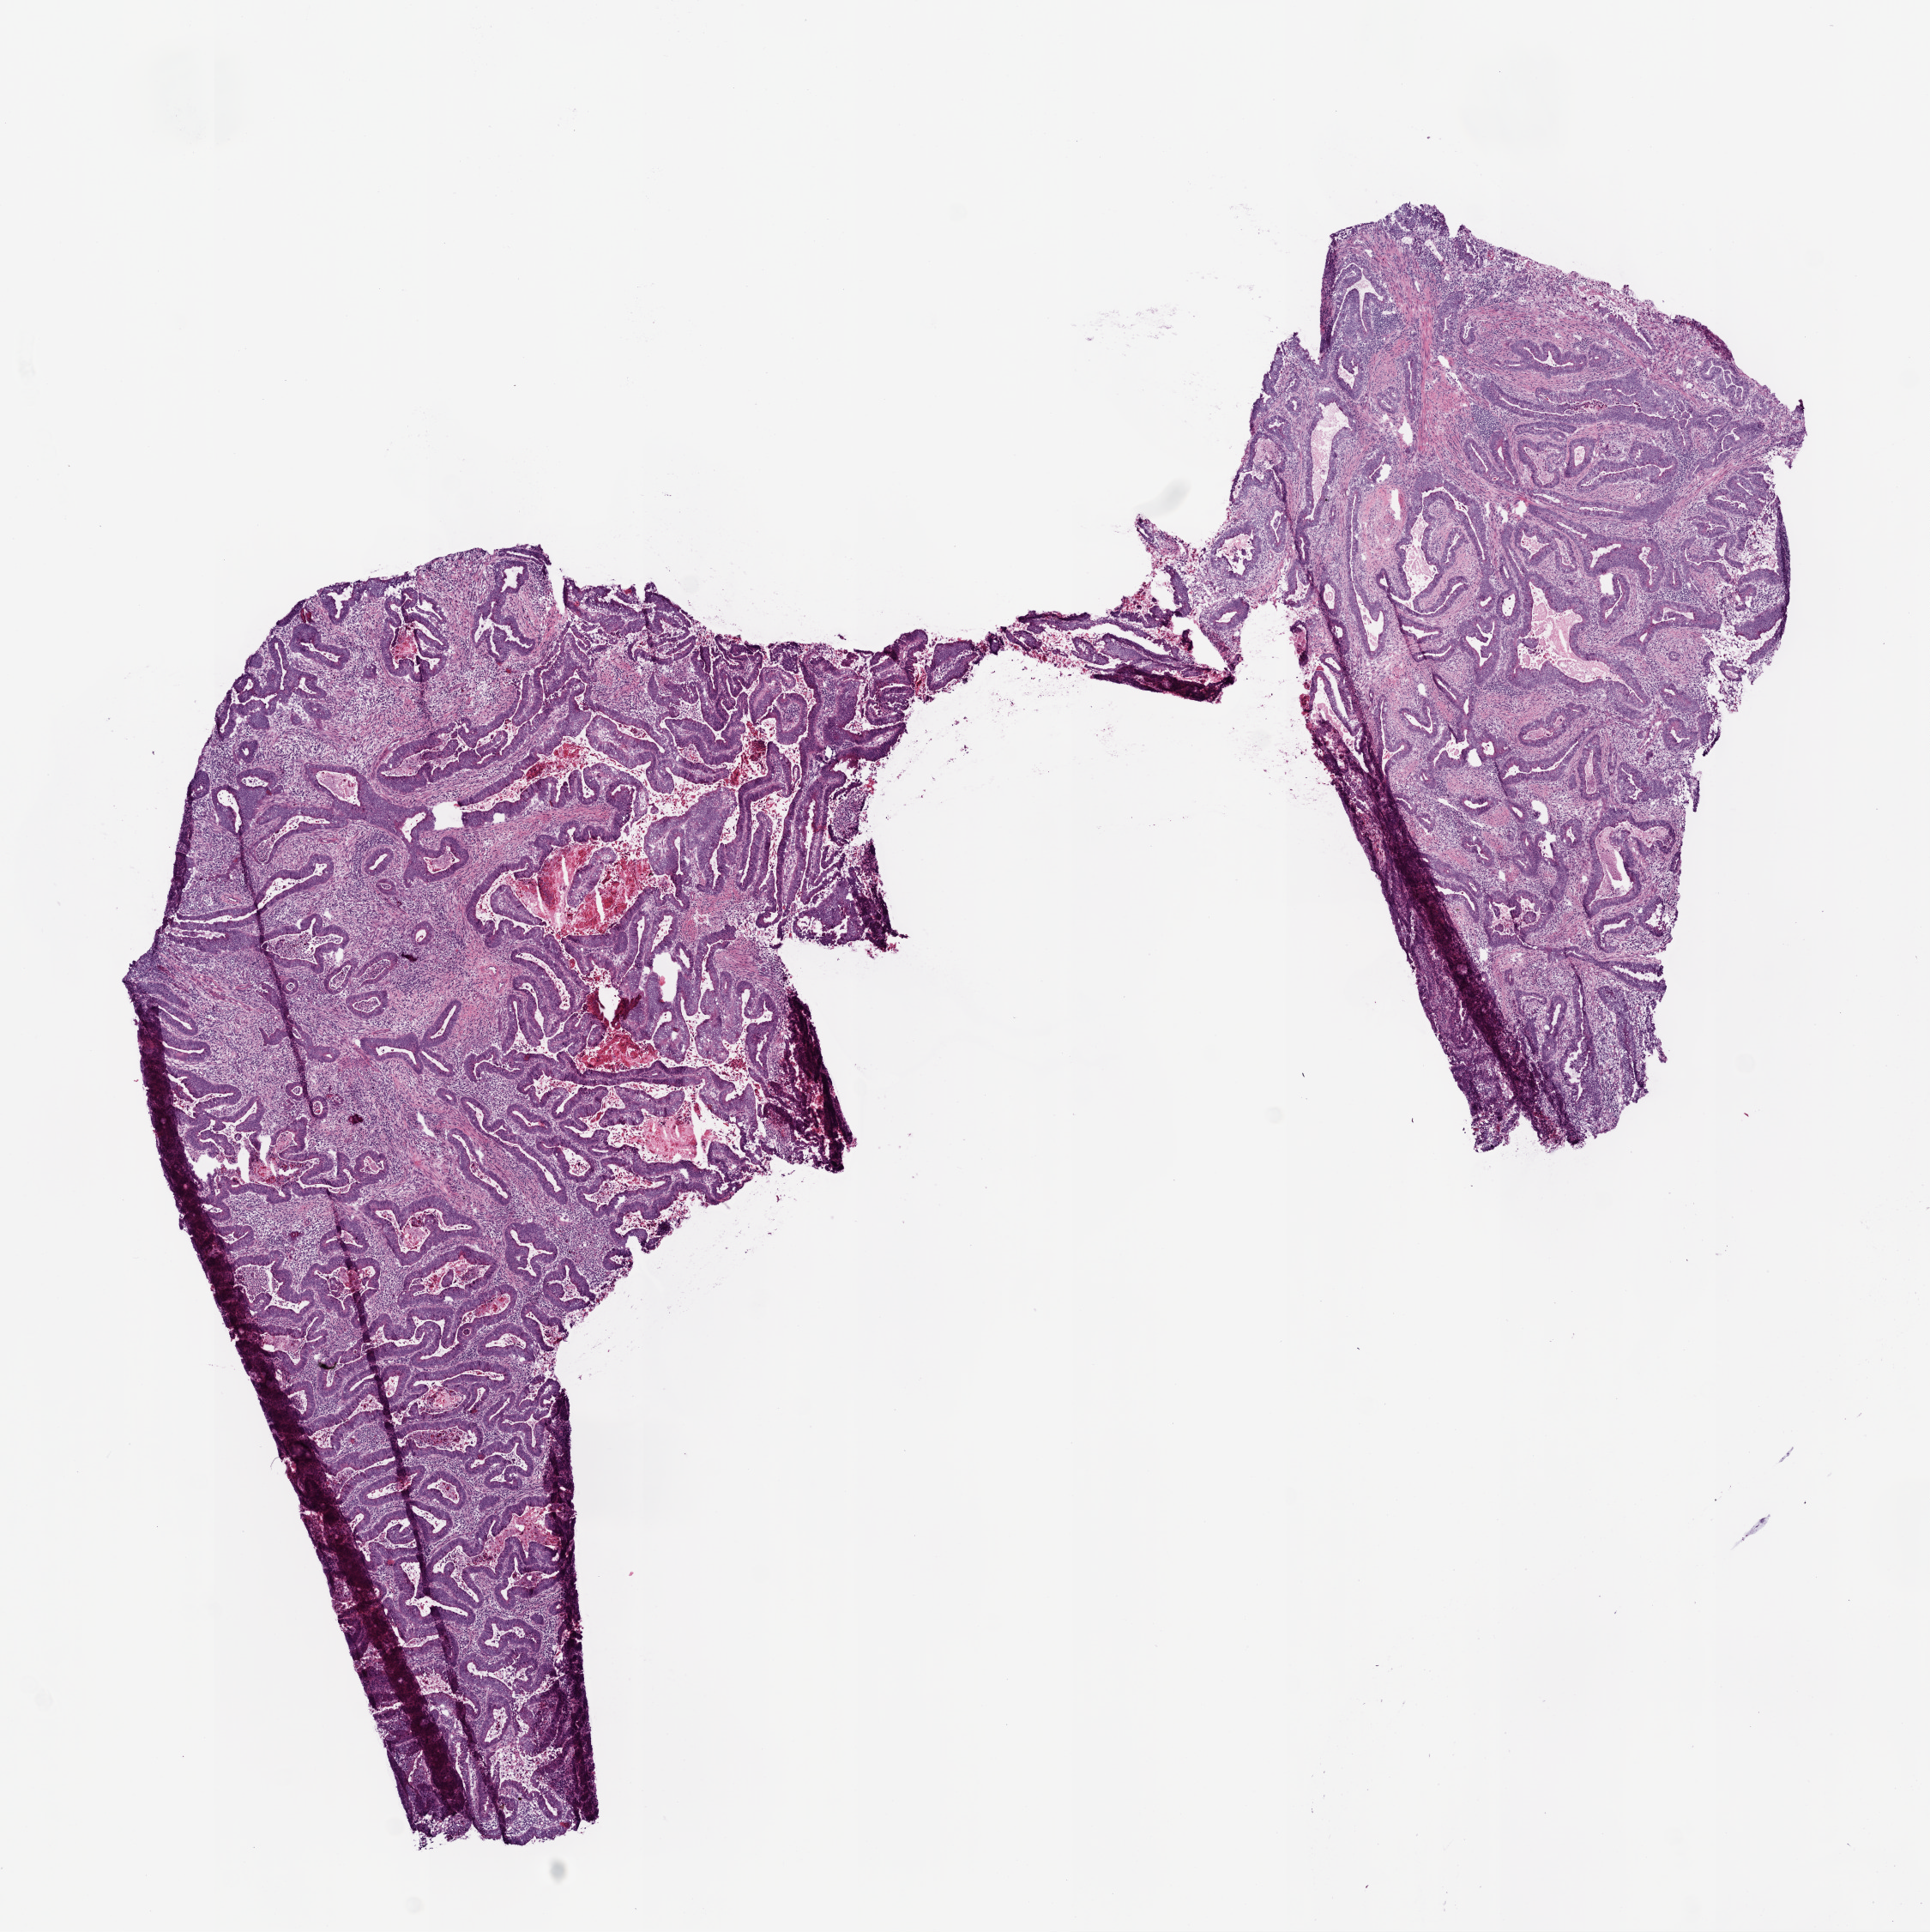
H&E-stained whole-slide image — shown as a low-resolution overview of the whole scanned area (about 9.0 x 9.0 mm); frozen section from the top of the tissue portion; primary tumour sample from the colon. Female, age 80 years at initial diagnosis. Pathologist review of this section (percent, as recorded): tumour cells 75%, tumour nuclei 65%, normal cells 0%, stromal cells 15%, necrosis 10%.
Lymph nodes positive (case pathology): 0 of 21 examined. Histologic diagnosis: Adenocarcinoma, NOS (sigmoid colon). AJCC pathologic stage: IIA. TNM: T3 N0 M0.